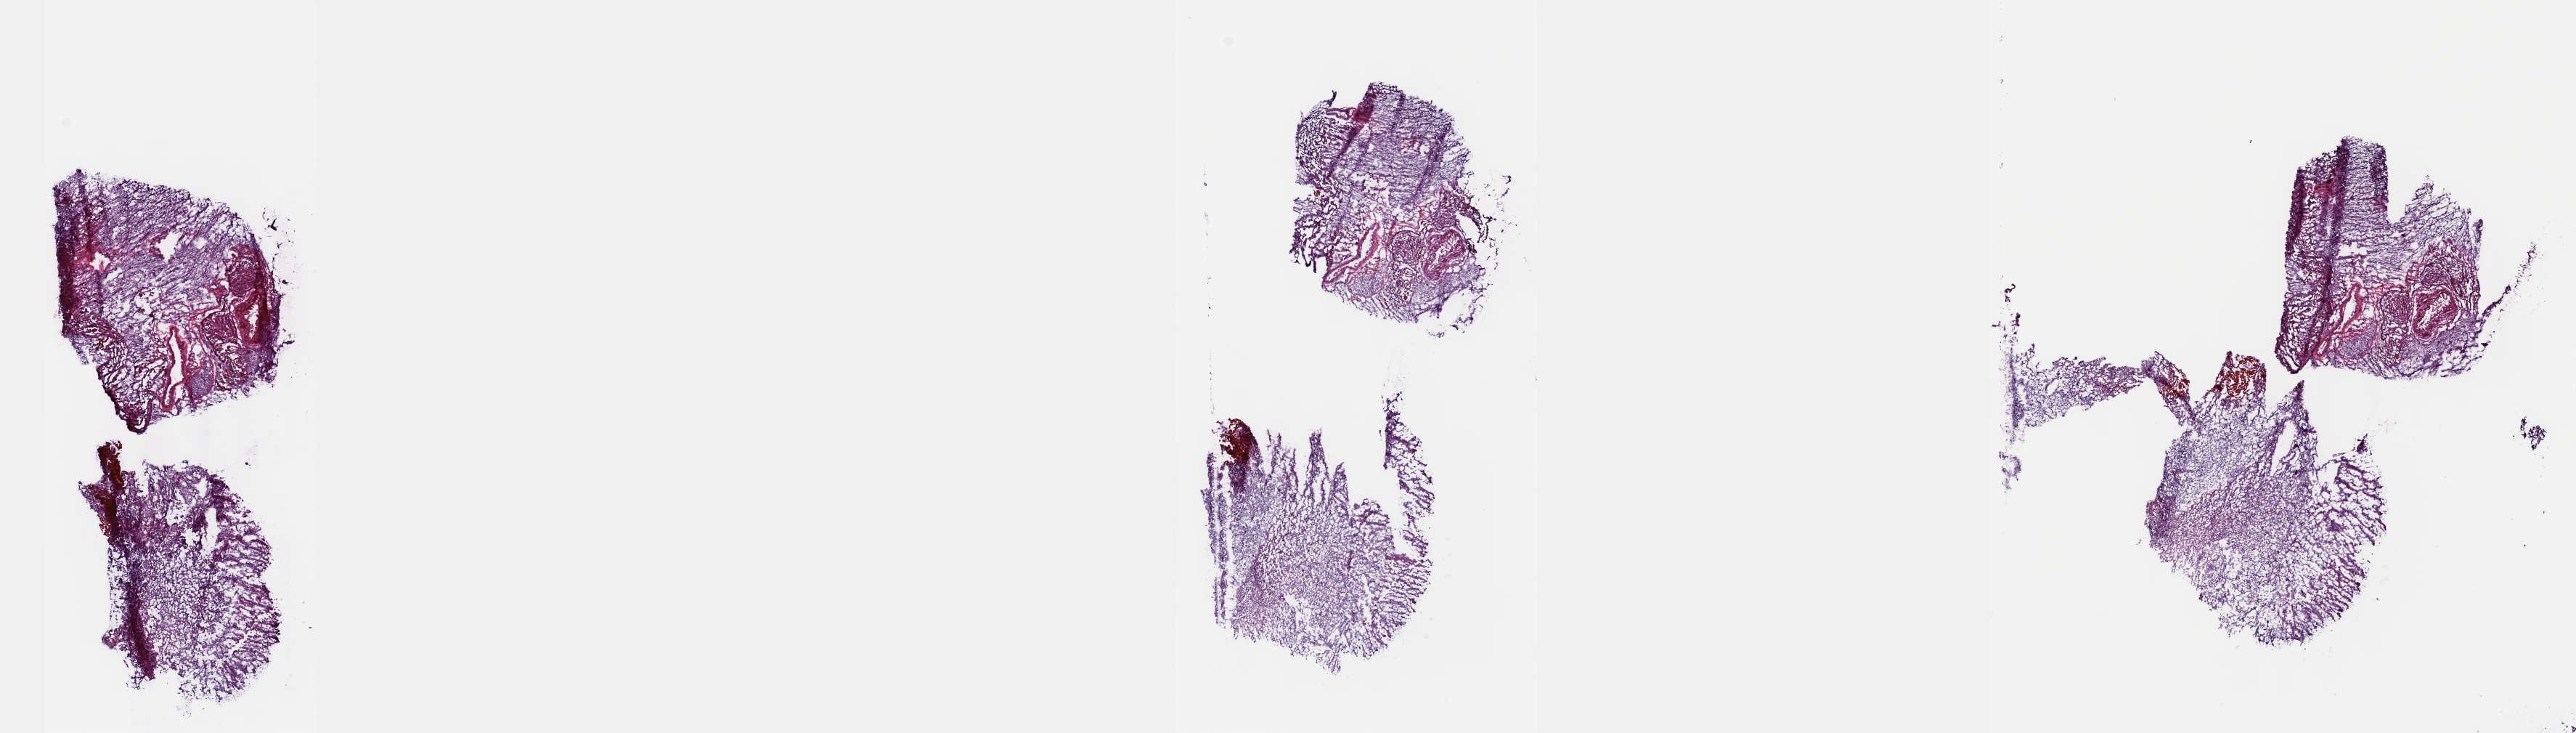
H&E-stained whole-slide image, whole scanned area (about 28.7 x 8.2 mm) shown as a low-resolution overview; frozen section; brain, primary tumour sample. Male, age 46 years at initial diagnosis. Histologic grade: G2 (moderately differentiated). Slide review estimates, as recorded: tumour cells 45%, tumour nuclei 70%, normal cells 10%, stromal cells 45%, necrosis 0%. Inflammatory infiltration, as recorded: lymphocyte infiltration 0%, monocyte infiltration 0%, neutrophil infiltration 0%.
Pathologic diagnosis: Oligodendroglioma, NOS.